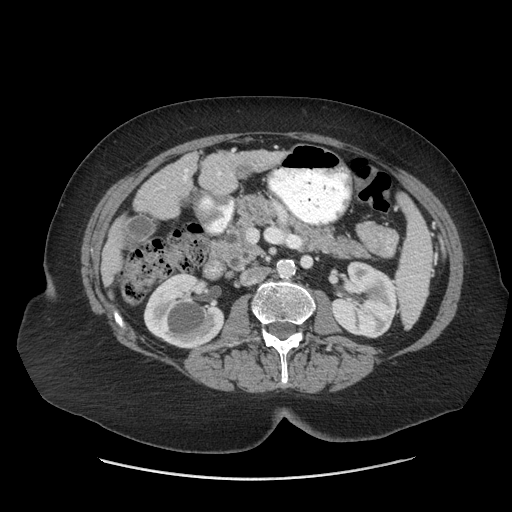
Contrast-enhanced abdominal CT (liver protocol), one axial slice. Slice 19 of 69 in the series (ordered by position). 140 kVp. Soft-tissue window (W 400 / L 40 HU). 2.5 mm slice thickness. 512 × 512 image matrix, field of view 420 × 420 mm. Case-level facts recorded for this patient, not image findings: diagnosis: hepatocellular carcinoma (patient treated with transarterial chemoembolisation; whether this scan precedes or follows treatment is not stated here); TNM stage (as recorded): Stage-IIIB; Child-Pugh class: A.
Structures marked on this image (semi-automatically segmented with operator editing):
- liver parenchyma outside the tumour (the mass and vessels are separate outlines, so this box may not span the whole liver): bounding box (x1, y1, x2, y2) in pixels: (102, 150, 284, 285)
- liver vessels: (218, 171, 222, 176)